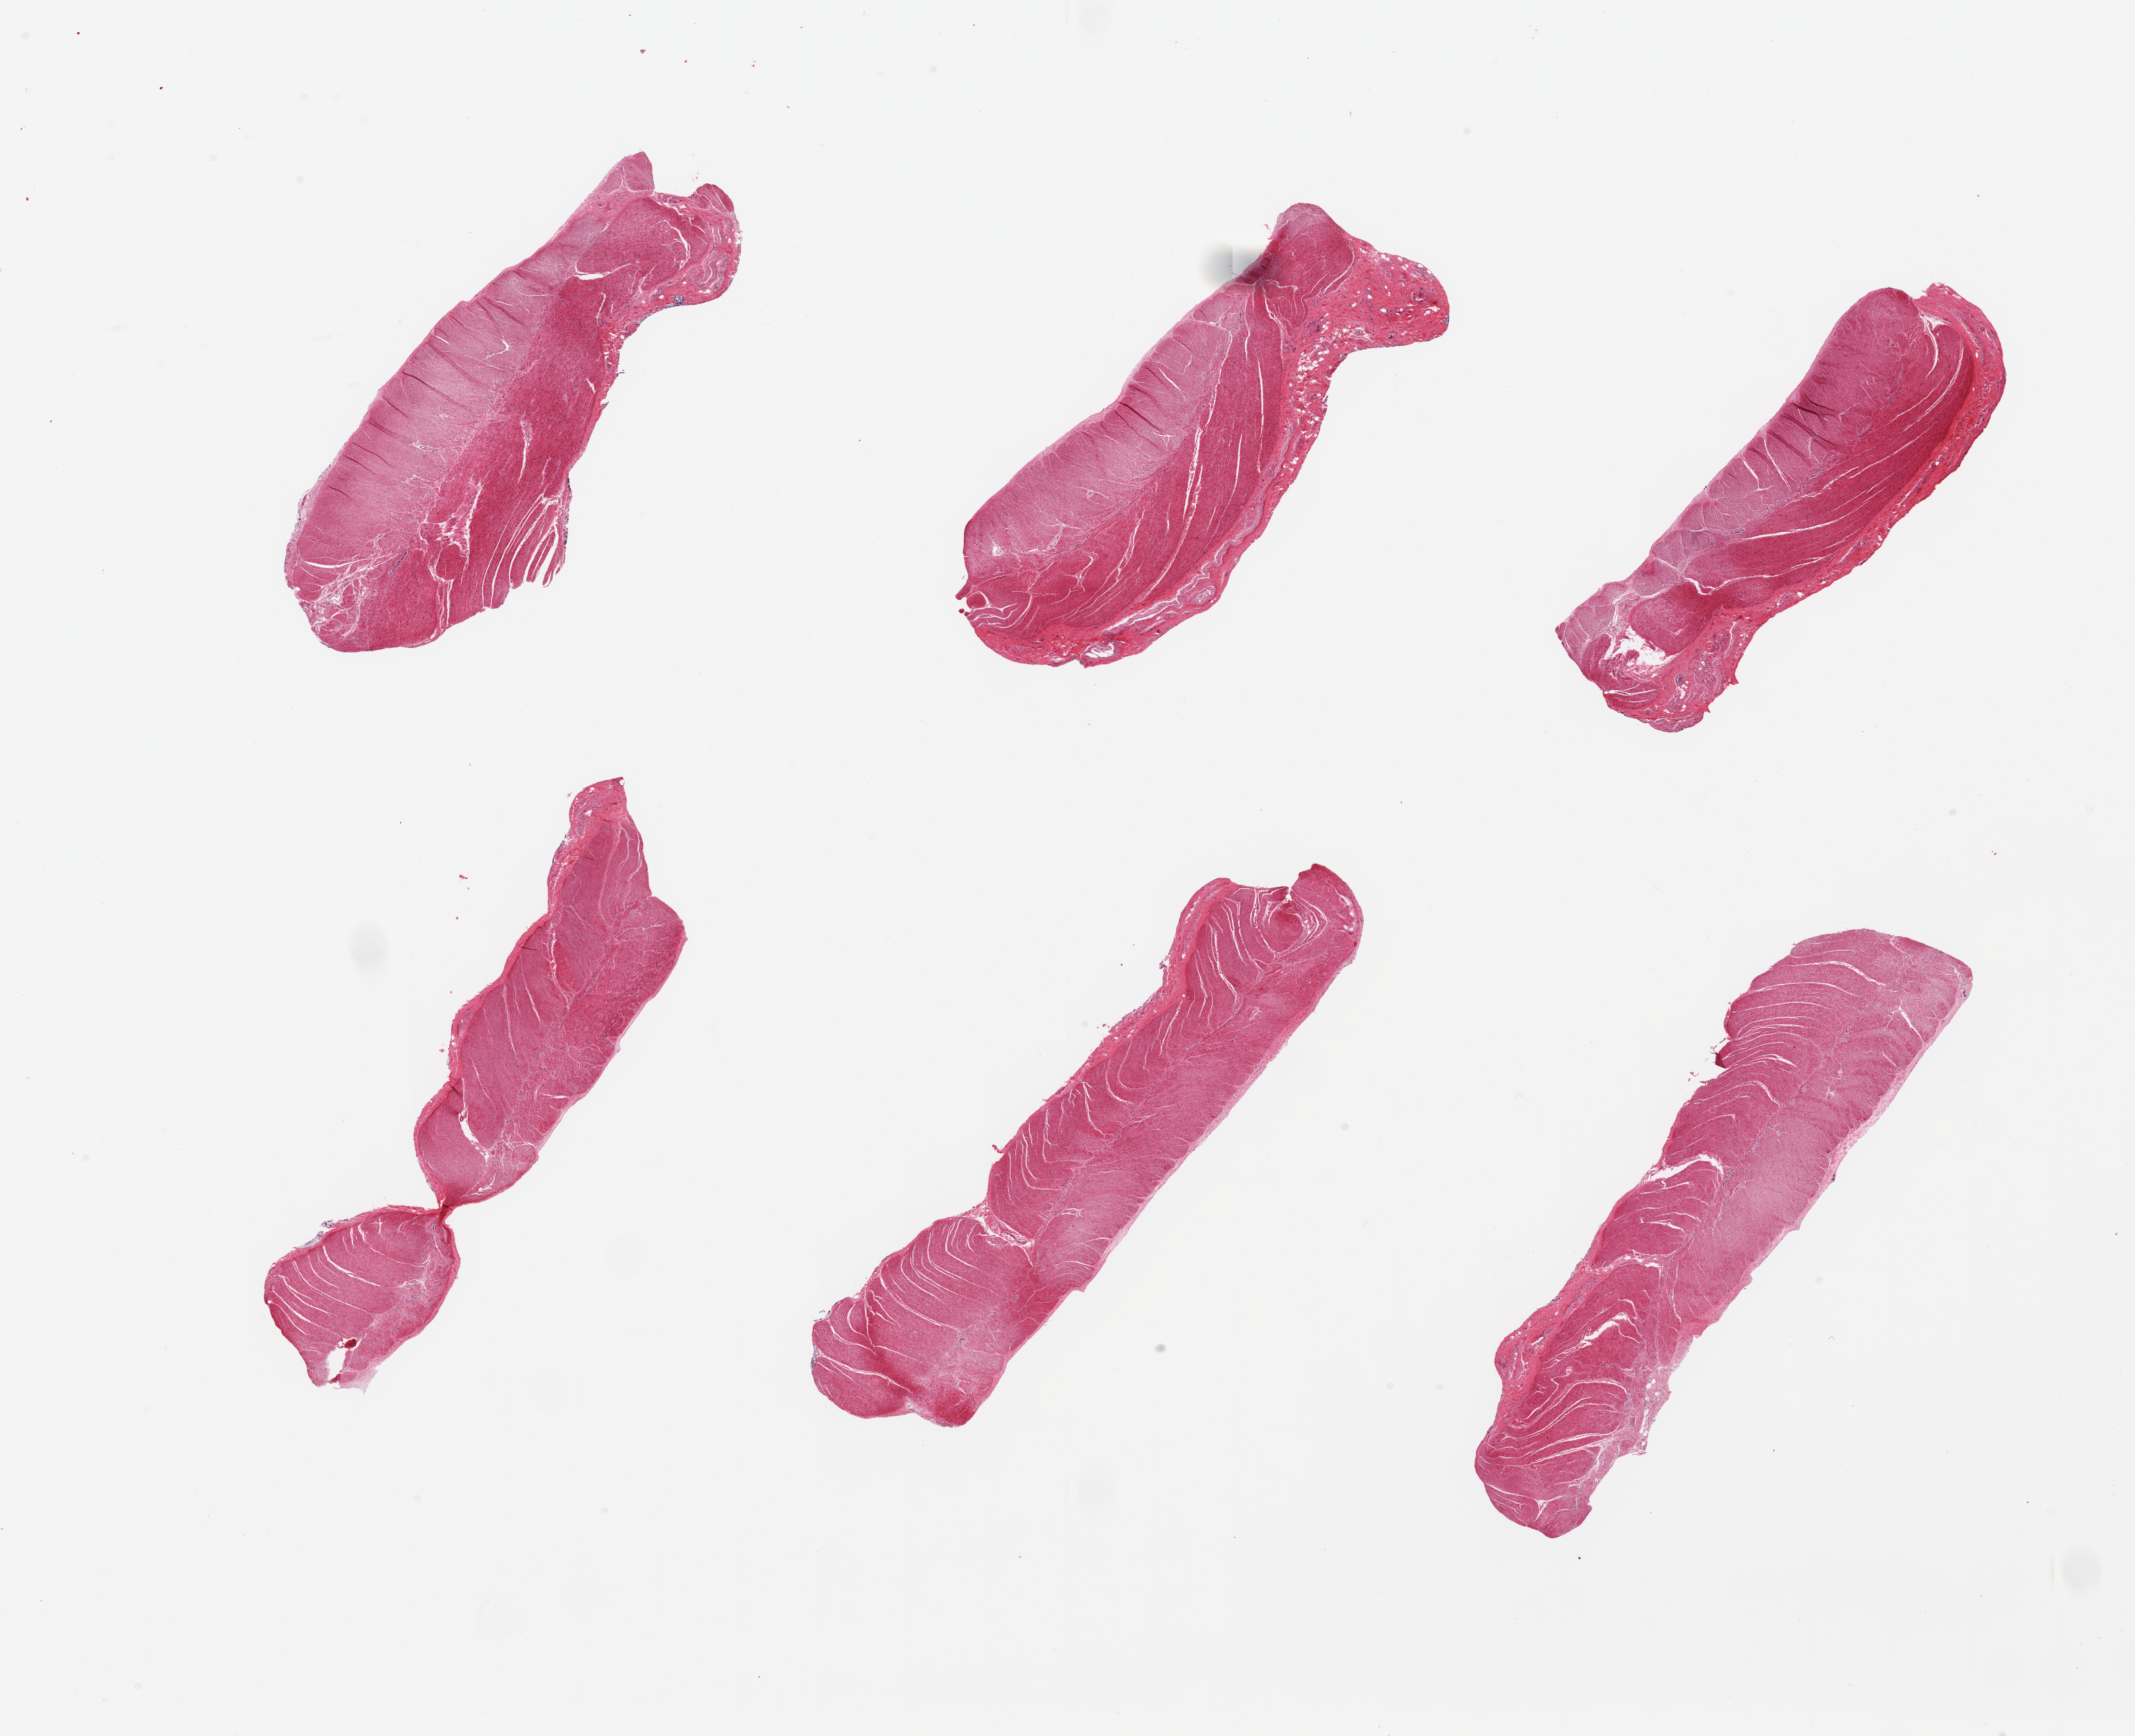
Digitized hematoxylin and eosin (H&E)-stained section, whole scanned area (about 25.6 x 20.8 mm, slide scanned at 20x) shown as a low-resolution overview. PAXgene-fixed paraffin-embedded (PFPE) section. Sampled site (target tissue): sigmoid colon. Donor tissue sample. Female donor.
• review note (as recorded): 6 pieces all muscularis